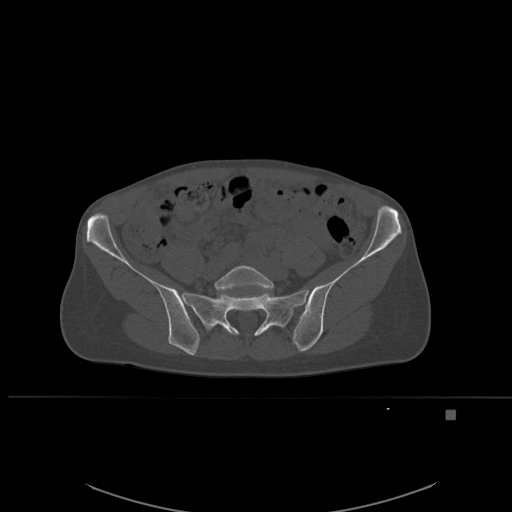
CT including the spine, one axial slice; slice 161 of 537 in the series (ordered by position); bone window (W 1800 / L 400 HU); 512 × 512 image matrix, field of view 440 × 440 mm. Patient: female, 45 years. From the clinical record (not read from this slice): primary cancer: lung.
Annotated regions visible in this slice (semi-automatic segmentation, software-assisted and operator-edited):
- L5 vertebra: bounding box [x1, y1, x2, y2] px = [214, 265, 274, 290]